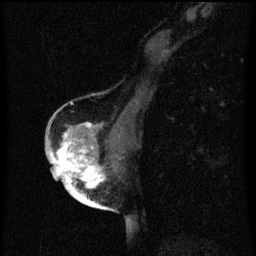
Breast MRI (dynamic contrast-enhanced), one sagittal slice. Slice 31 of 60 in the series (ordered by position). Dynamic contrast-enhanced series, image 2 of 3 at this slice position (ordered by acquisition). 1.5 T. TE 4.2 ms, TR 8 ms. 256 × 256 image matrix, field of view 180 × 180 mm. Female patient, age 56 years.
Structures marked on this image (semi-automatic segmentation, software-assisted and operator-edited):
- analysis volume of interest (the breast-tissue region the enhancement analysis was run in; not a lesion): bounding box [x1, y1, x2, y2] px = [54, 124, 119, 199]
- tumour enhancement mask (voxels above the 70 % enhancement threshold inside the analysis volume of interest): [54, 124, 106, 199]